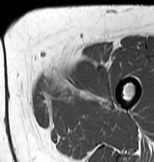
MRI of an extremity soft-tissue mass, one axial slice; position 16 of 83 along the scan axis; MR volume resampled by the dataset authors to the PET/CT grid (not the native acquisition matrix); 3.27 mm slice thickness; 154 × 162 image matrix, field of view 150 × 158 mm. Female patient. From the clinical record (not read from this slice): histological type: myxofibrosarcoma; grade: intermediate; site of the primary tumour: left thigh.
Annotated regions visible in this slice (expert contour drawn on MRI and transferred to this co-registered scan by the dataset authors):
- gross tumour volume including surrounding oedema: bounding box (x1, y1, x2, y2) in pixels: (37, 63, 113, 112)
- gross tumour volume (mass): (47, 63, 102, 97)